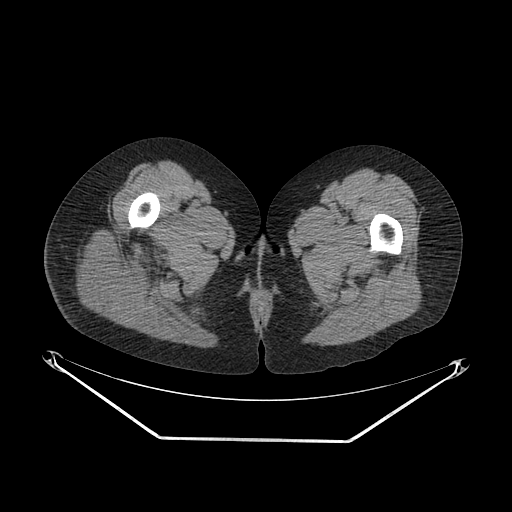
CT of an extremity soft-tissue mass (from a PET/CT study), one axial slice. Position 27 of 267 along the scan axis. 140 kVp. Soft-tissue window (W 400 / L 40 HU). 3.75 mm slice thickness. 512 × 512 image matrix, field of view 500 × 500 mm. Female patient. Case-level facts recorded for this patient, not image findings: histological type: epithelioid sarcoma with vascular differentiation; site of the primary tumour: right buttock.
Annotated regions visible in this slice (expert contour drawn on MRI and transferred to this co-registered scan by the dataset authors):
- gross tumour volume (mass): bounding box [x1, y1, x2, y2] px = [77, 237, 131, 312]